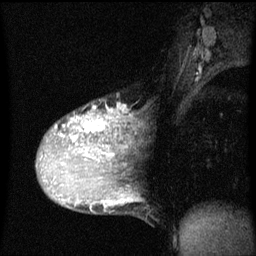
Breast MRI (dynamic contrast-enhanced), one sagittal slice. Slice 35 of 60 in the series (ordered by position). Dynamic contrast-enhanced series, image 2 of 3 at this slice position (ordered by acquisition). 1.5 T. TE 4.2 ms, TR 8 ms. 2 mm slice thickness. 256 × 256 image matrix. Female patient, age 36 years.
Annotated regions visible in this slice (semi-automatically segmented with operator editing):
- analysis volume of interest (the breast-tissue region the enhancement analysis was run in; not a lesion): bounding box (x1, y1, x2, y2) in pixels: (37, 106, 124, 169)
- tumour enhancement mask (voxels above the 70 % enhancement threshold inside the analysis volume of interest): (54, 106, 124, 167)